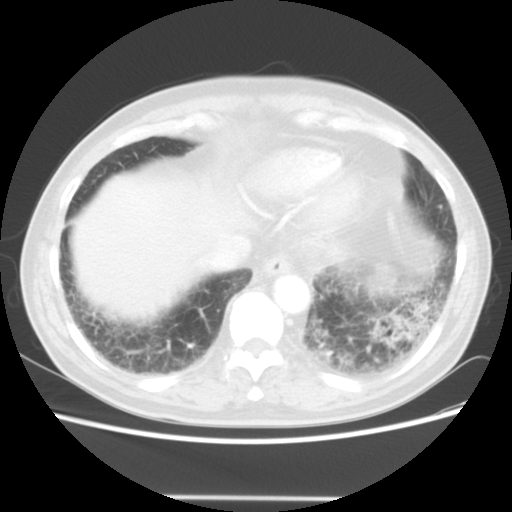
Chest CT, one axial slice; position 11 of 56 along the scan axis; lung window (W 1500 / L -600 HU); 5 mm slice thickness; 512 × 512 image matrix. Patient: male, 66 years. Case-level facts recorded for this patient, not image findings: clinical TNM (as recorded): T4 N3 M0; histopathological grade: G3.
Structures marked on this image (rectangle marked by the reading radiologist):
- lung tumour (recorded histology: small cell carcinoma): bounding box [x1, y1, x2, y2] px = [364, 259, 401, 299]